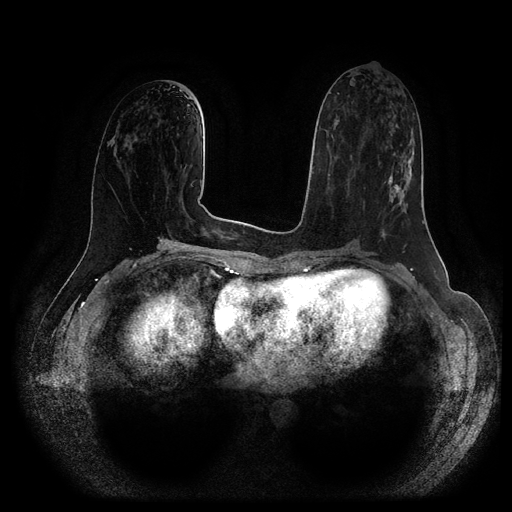
Breast MRI (dynamic contrast-enhanced, multi-phase), one axial slice; position 47 of 116 along the scan axis; dynamic contrast-enhanced series, time point 2 of 5 at this slice position (early post-contrast); 1.5 T; TE 2.6 ms, TR 5.2 ms; 512 × 512 image matrix, field of view 380 × 380 mm. Female patient, age 57 years.
Outlined on this slice (semi-automatic segmentation, software-assisted and operator-edited):
- breast lesion (labelled 'tumour' in the annotation; benign lesions carry a separate 'benign' label): bounding box [x1, y1, x2, y2] px = [384, 150, 415, 208]